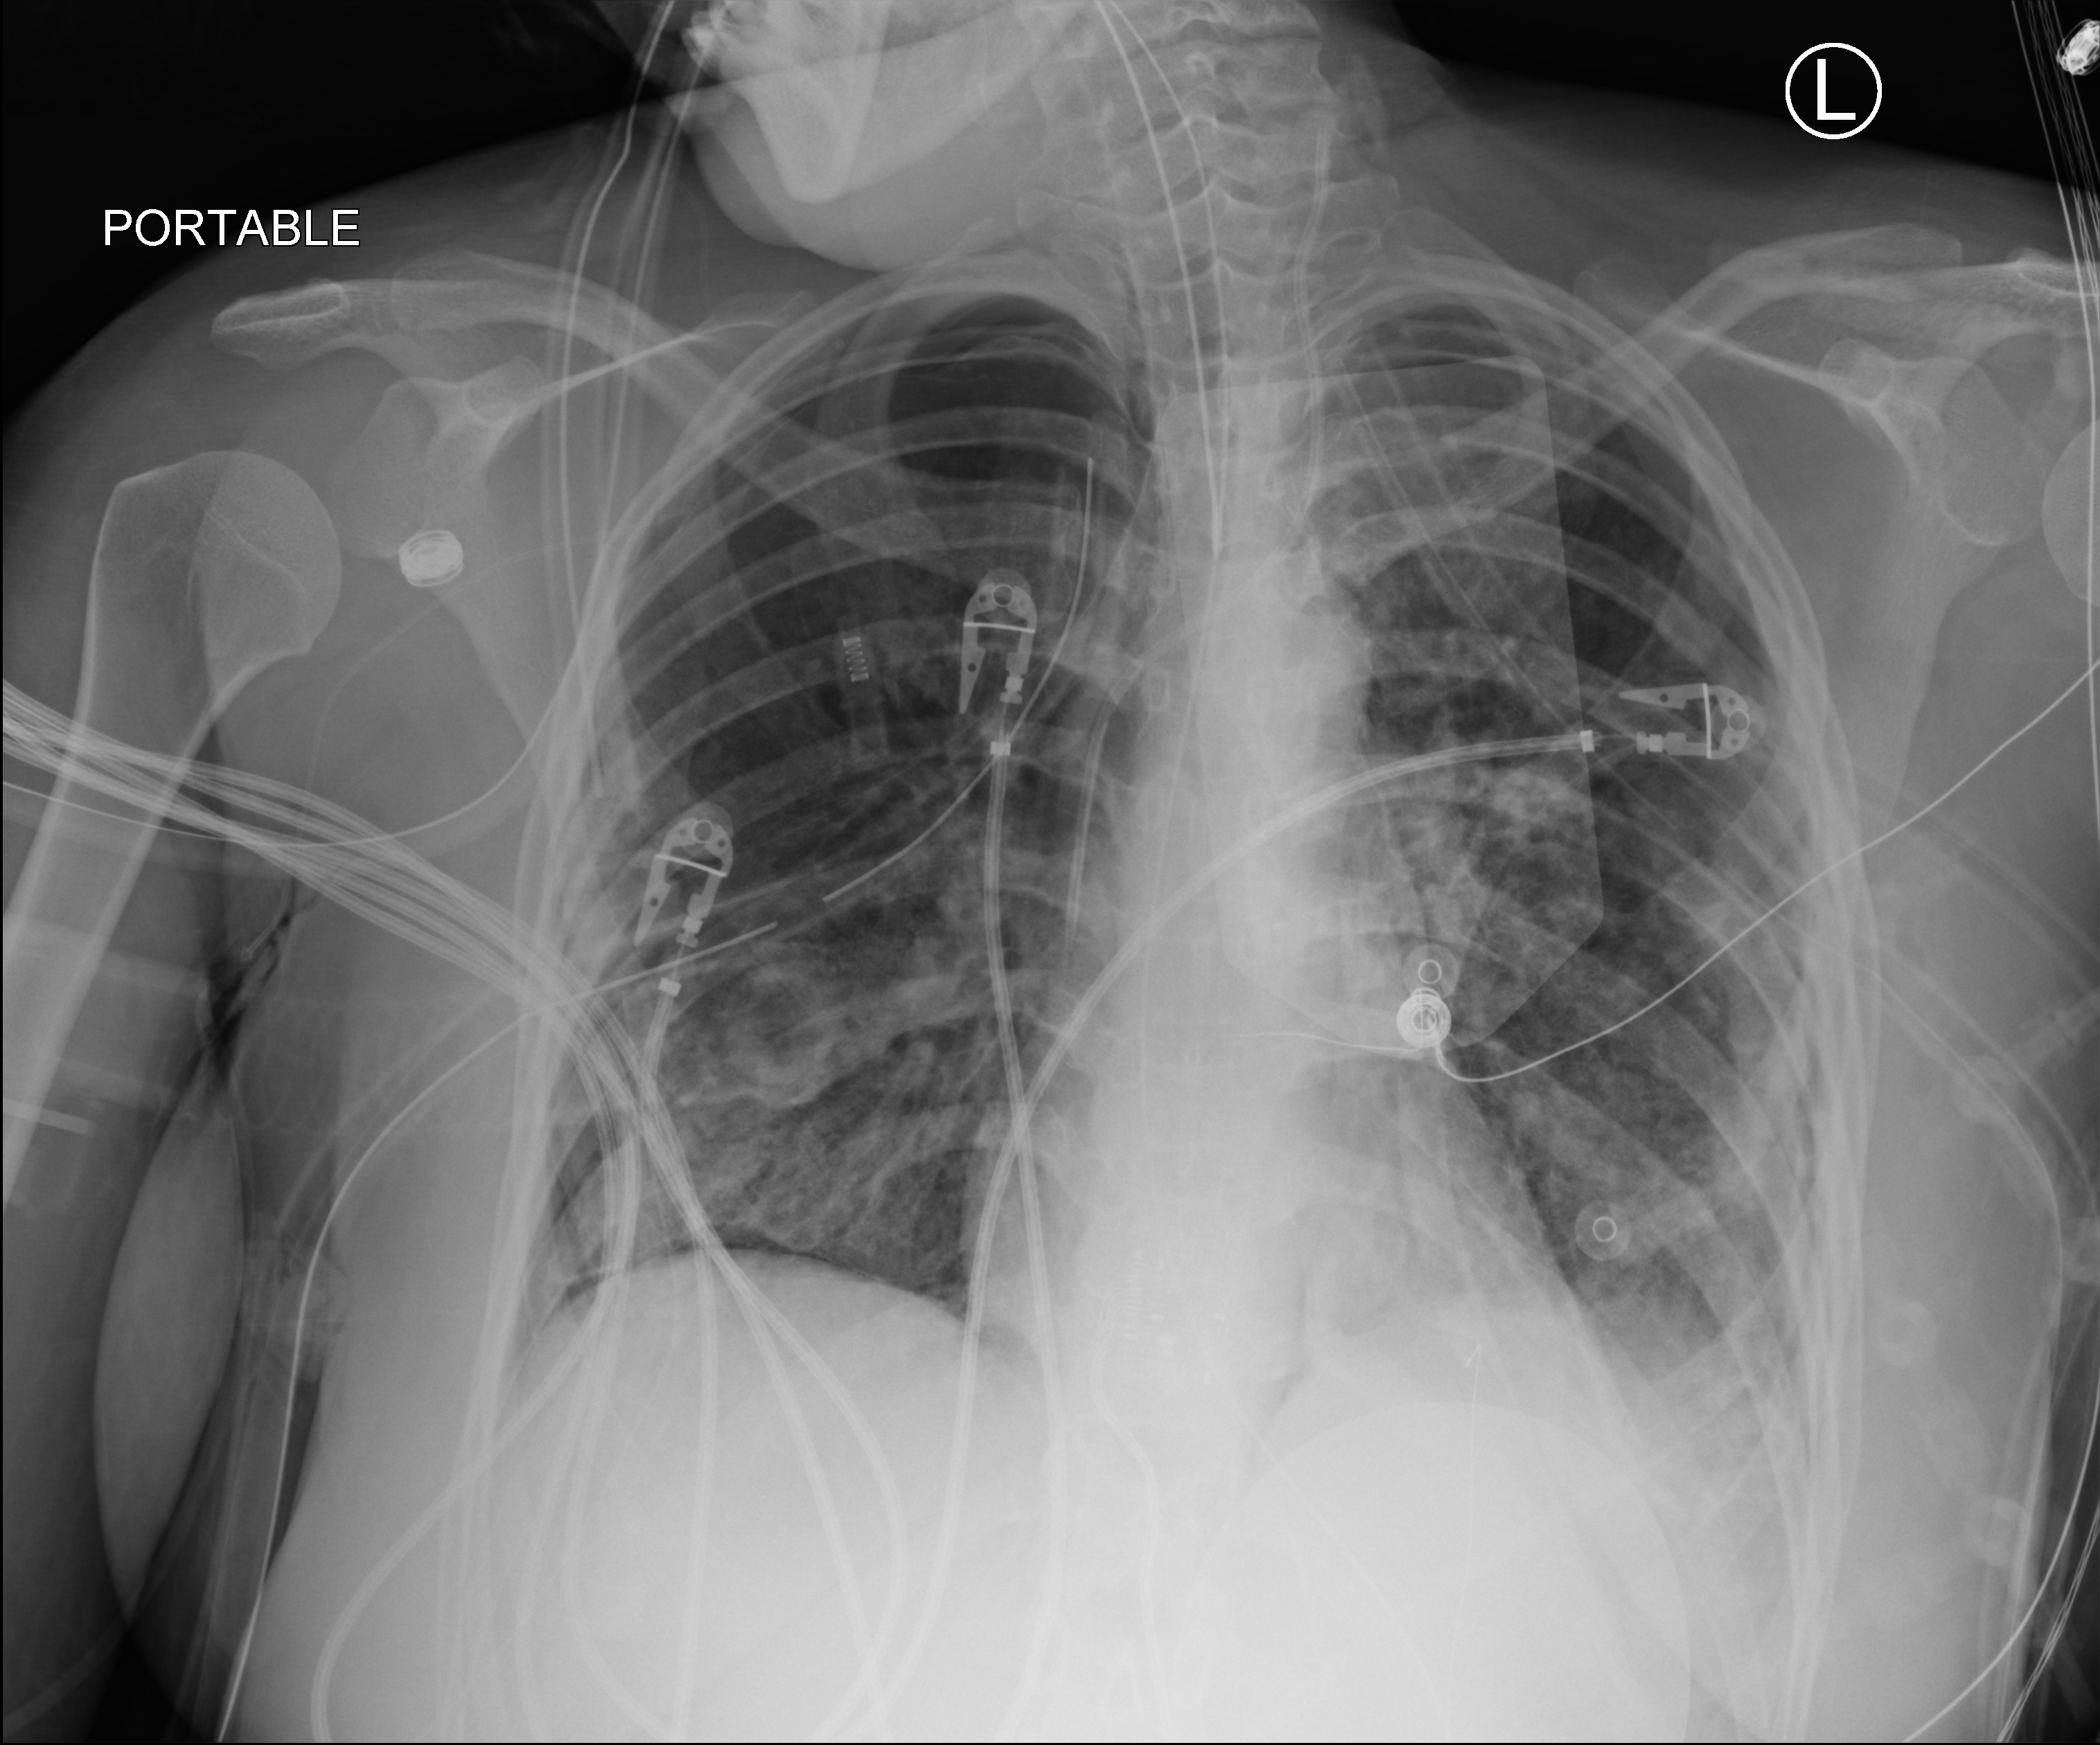
Chest X-ray (portable); anteroposterior (AP) projection. Patient hospitalised with COVID-19, aged 18–59 years.
From the hospital-stay record, not from the radiograph (when in the stay this image was taken is not recorded):
- hypertension (admission record): no
- admitted to intensive care during this hospital stay: yes